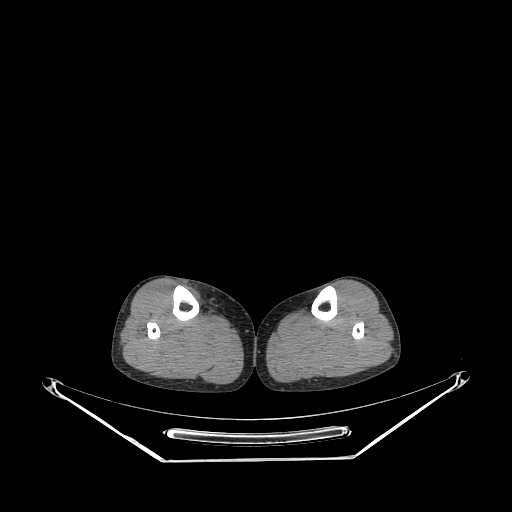
CT of an extremity soft-tissue mass (from a PET/CT study), one axial slice; slice 131 of 267 in the series (ordered by position); reconstruction kernel STANDARD; 140 kVp; soft-tissue window (W 400 / L 40 HU); 512 × 512 image matrix, field of view 500 × 500 mm. Female patient. Case-level facts recorded for this patient, not image findings: histological type: undifferentiated – high grade; grade: high; site of the primary tumour: right thigh.
Outlined on this slice (expert contour drawn on MRI and transferred to this co-registered scan by the dataset authors):
- gross tumour volume (mass): bounding box [x1, y1, x2, y2] px = [187, 288, 202, 305]